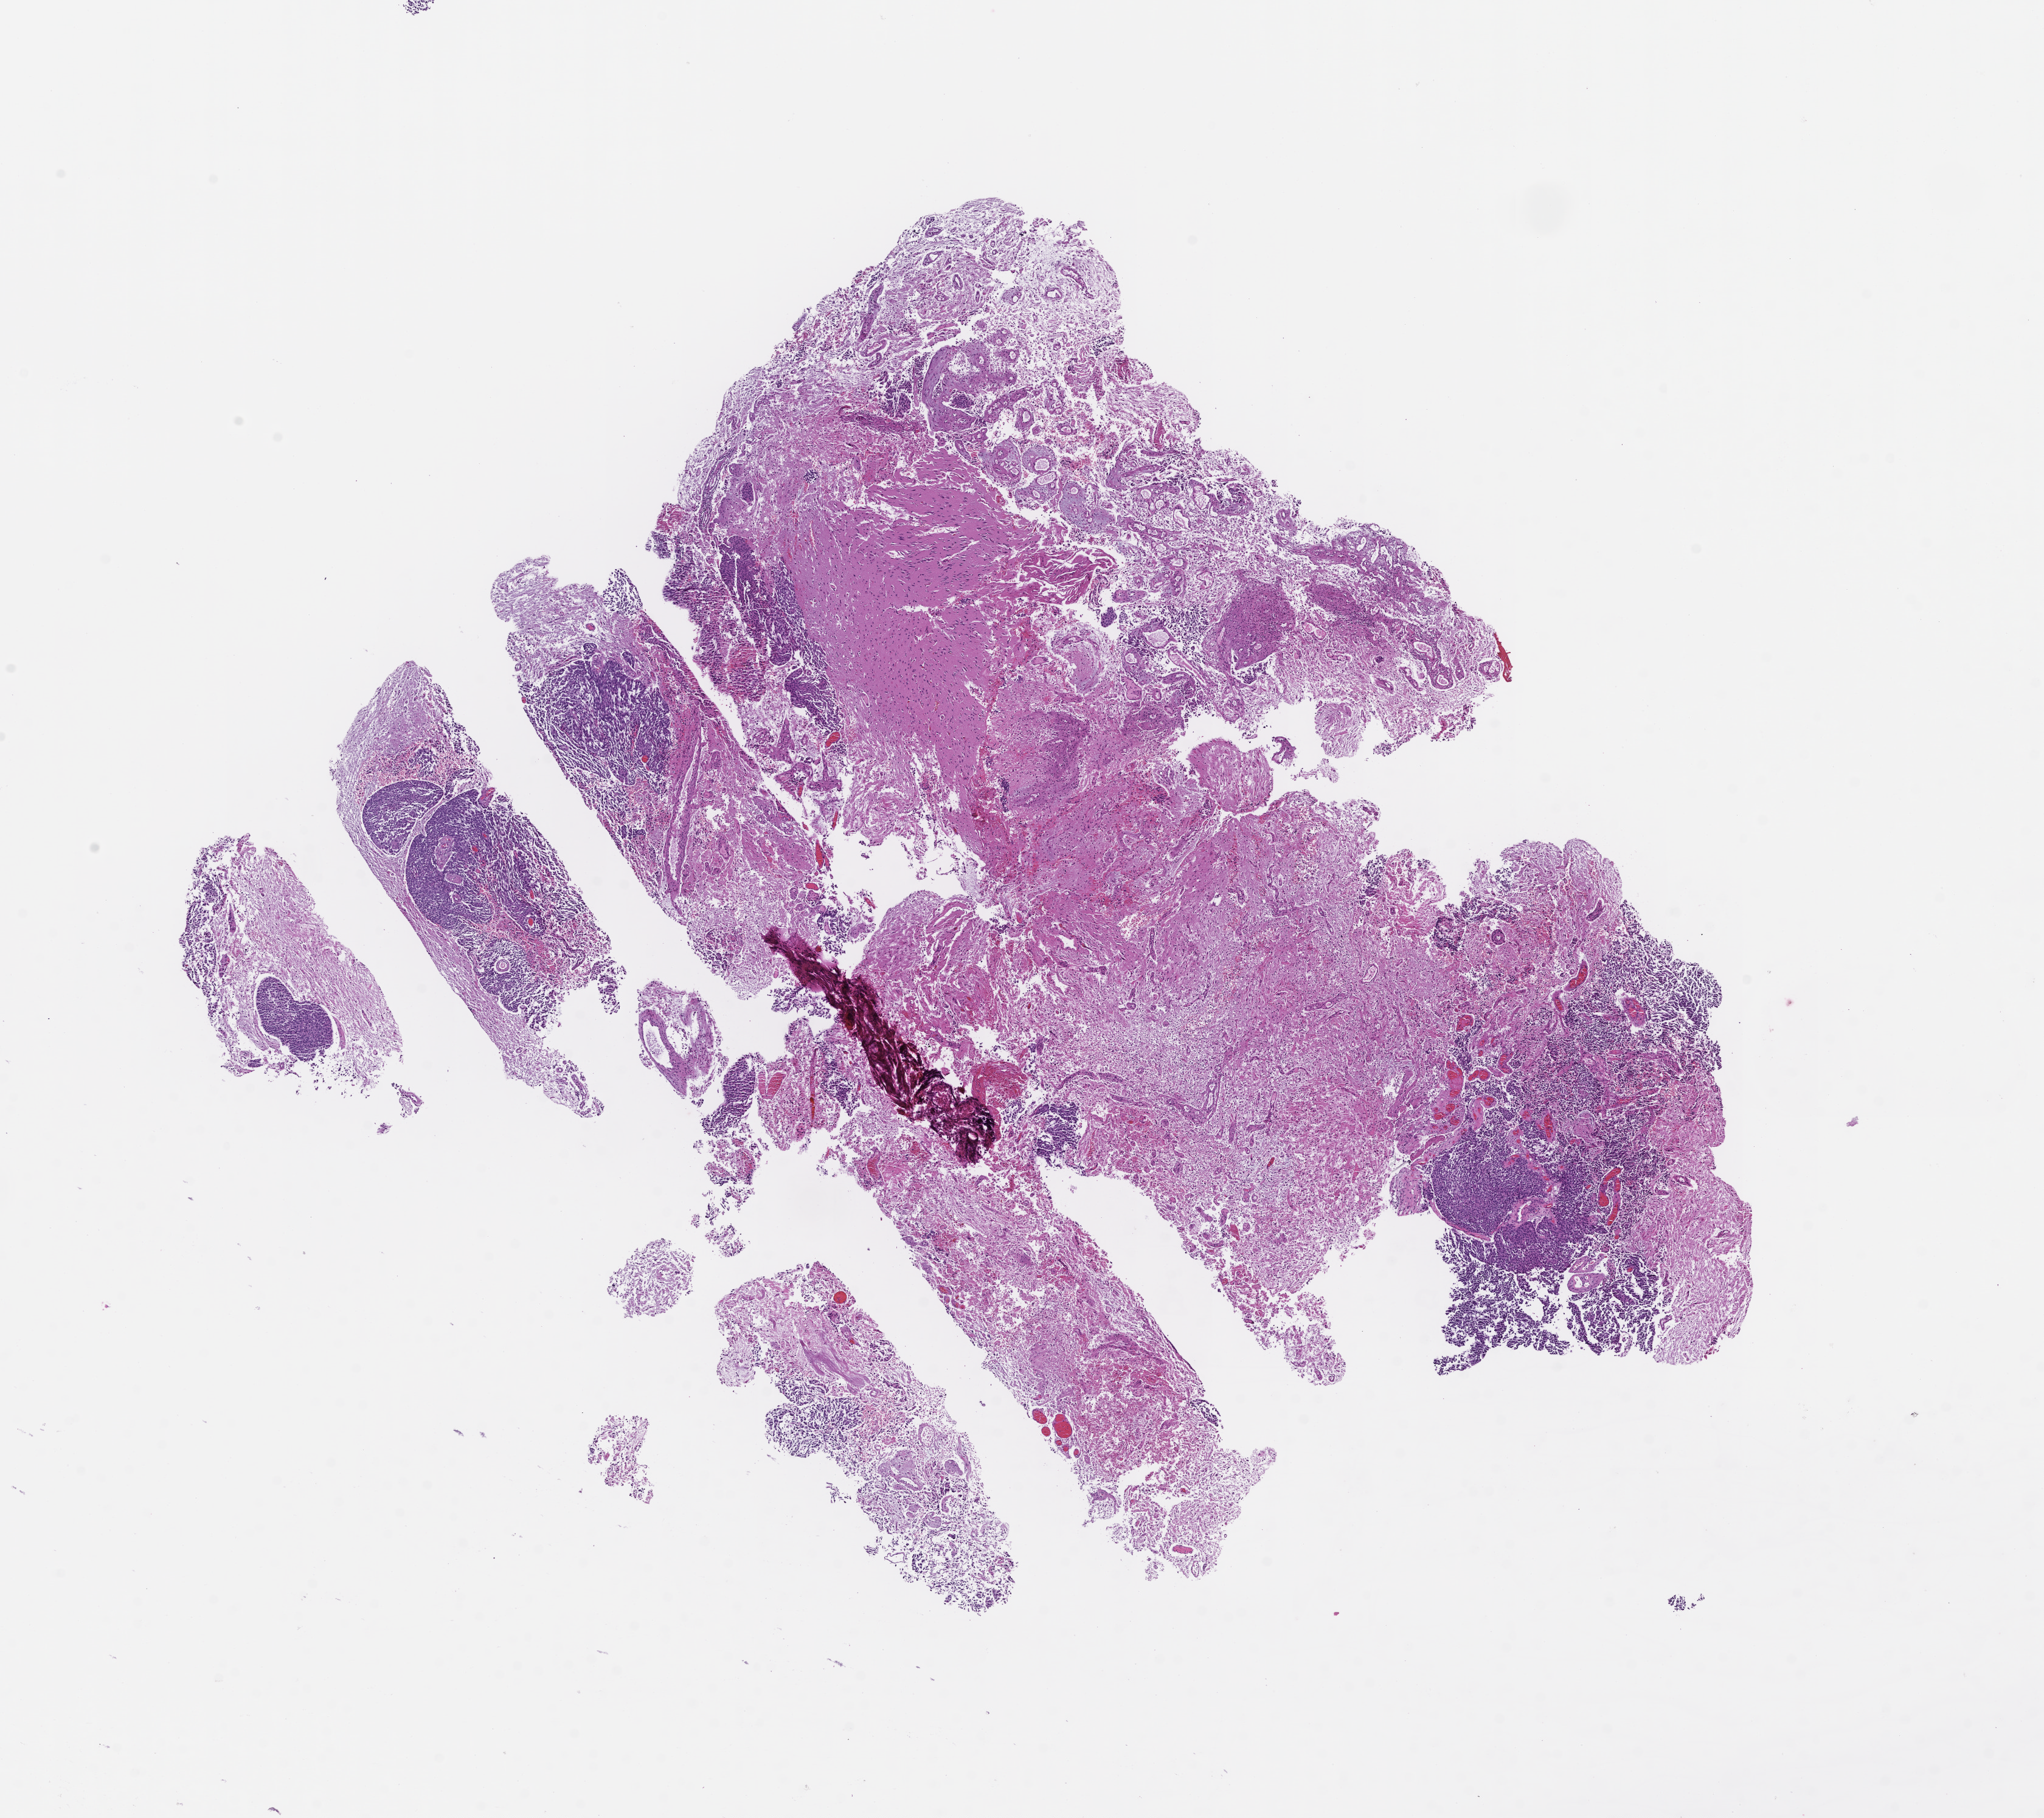
Whole-slide image, hematoxylin and eosin (H&E) stain, whole scanned area (about 13.6 x 12.1 mm) shown as a low-resolution overview. Formalin-fixed, paraffin-embedded (FFPE) tissue. Specimen time point: collected at baseline (before treatment). Patient: male.
This section: metastatic tumor tissue. Patient diagnosis (primary): Non-Small Cell Lung Carcinoma.